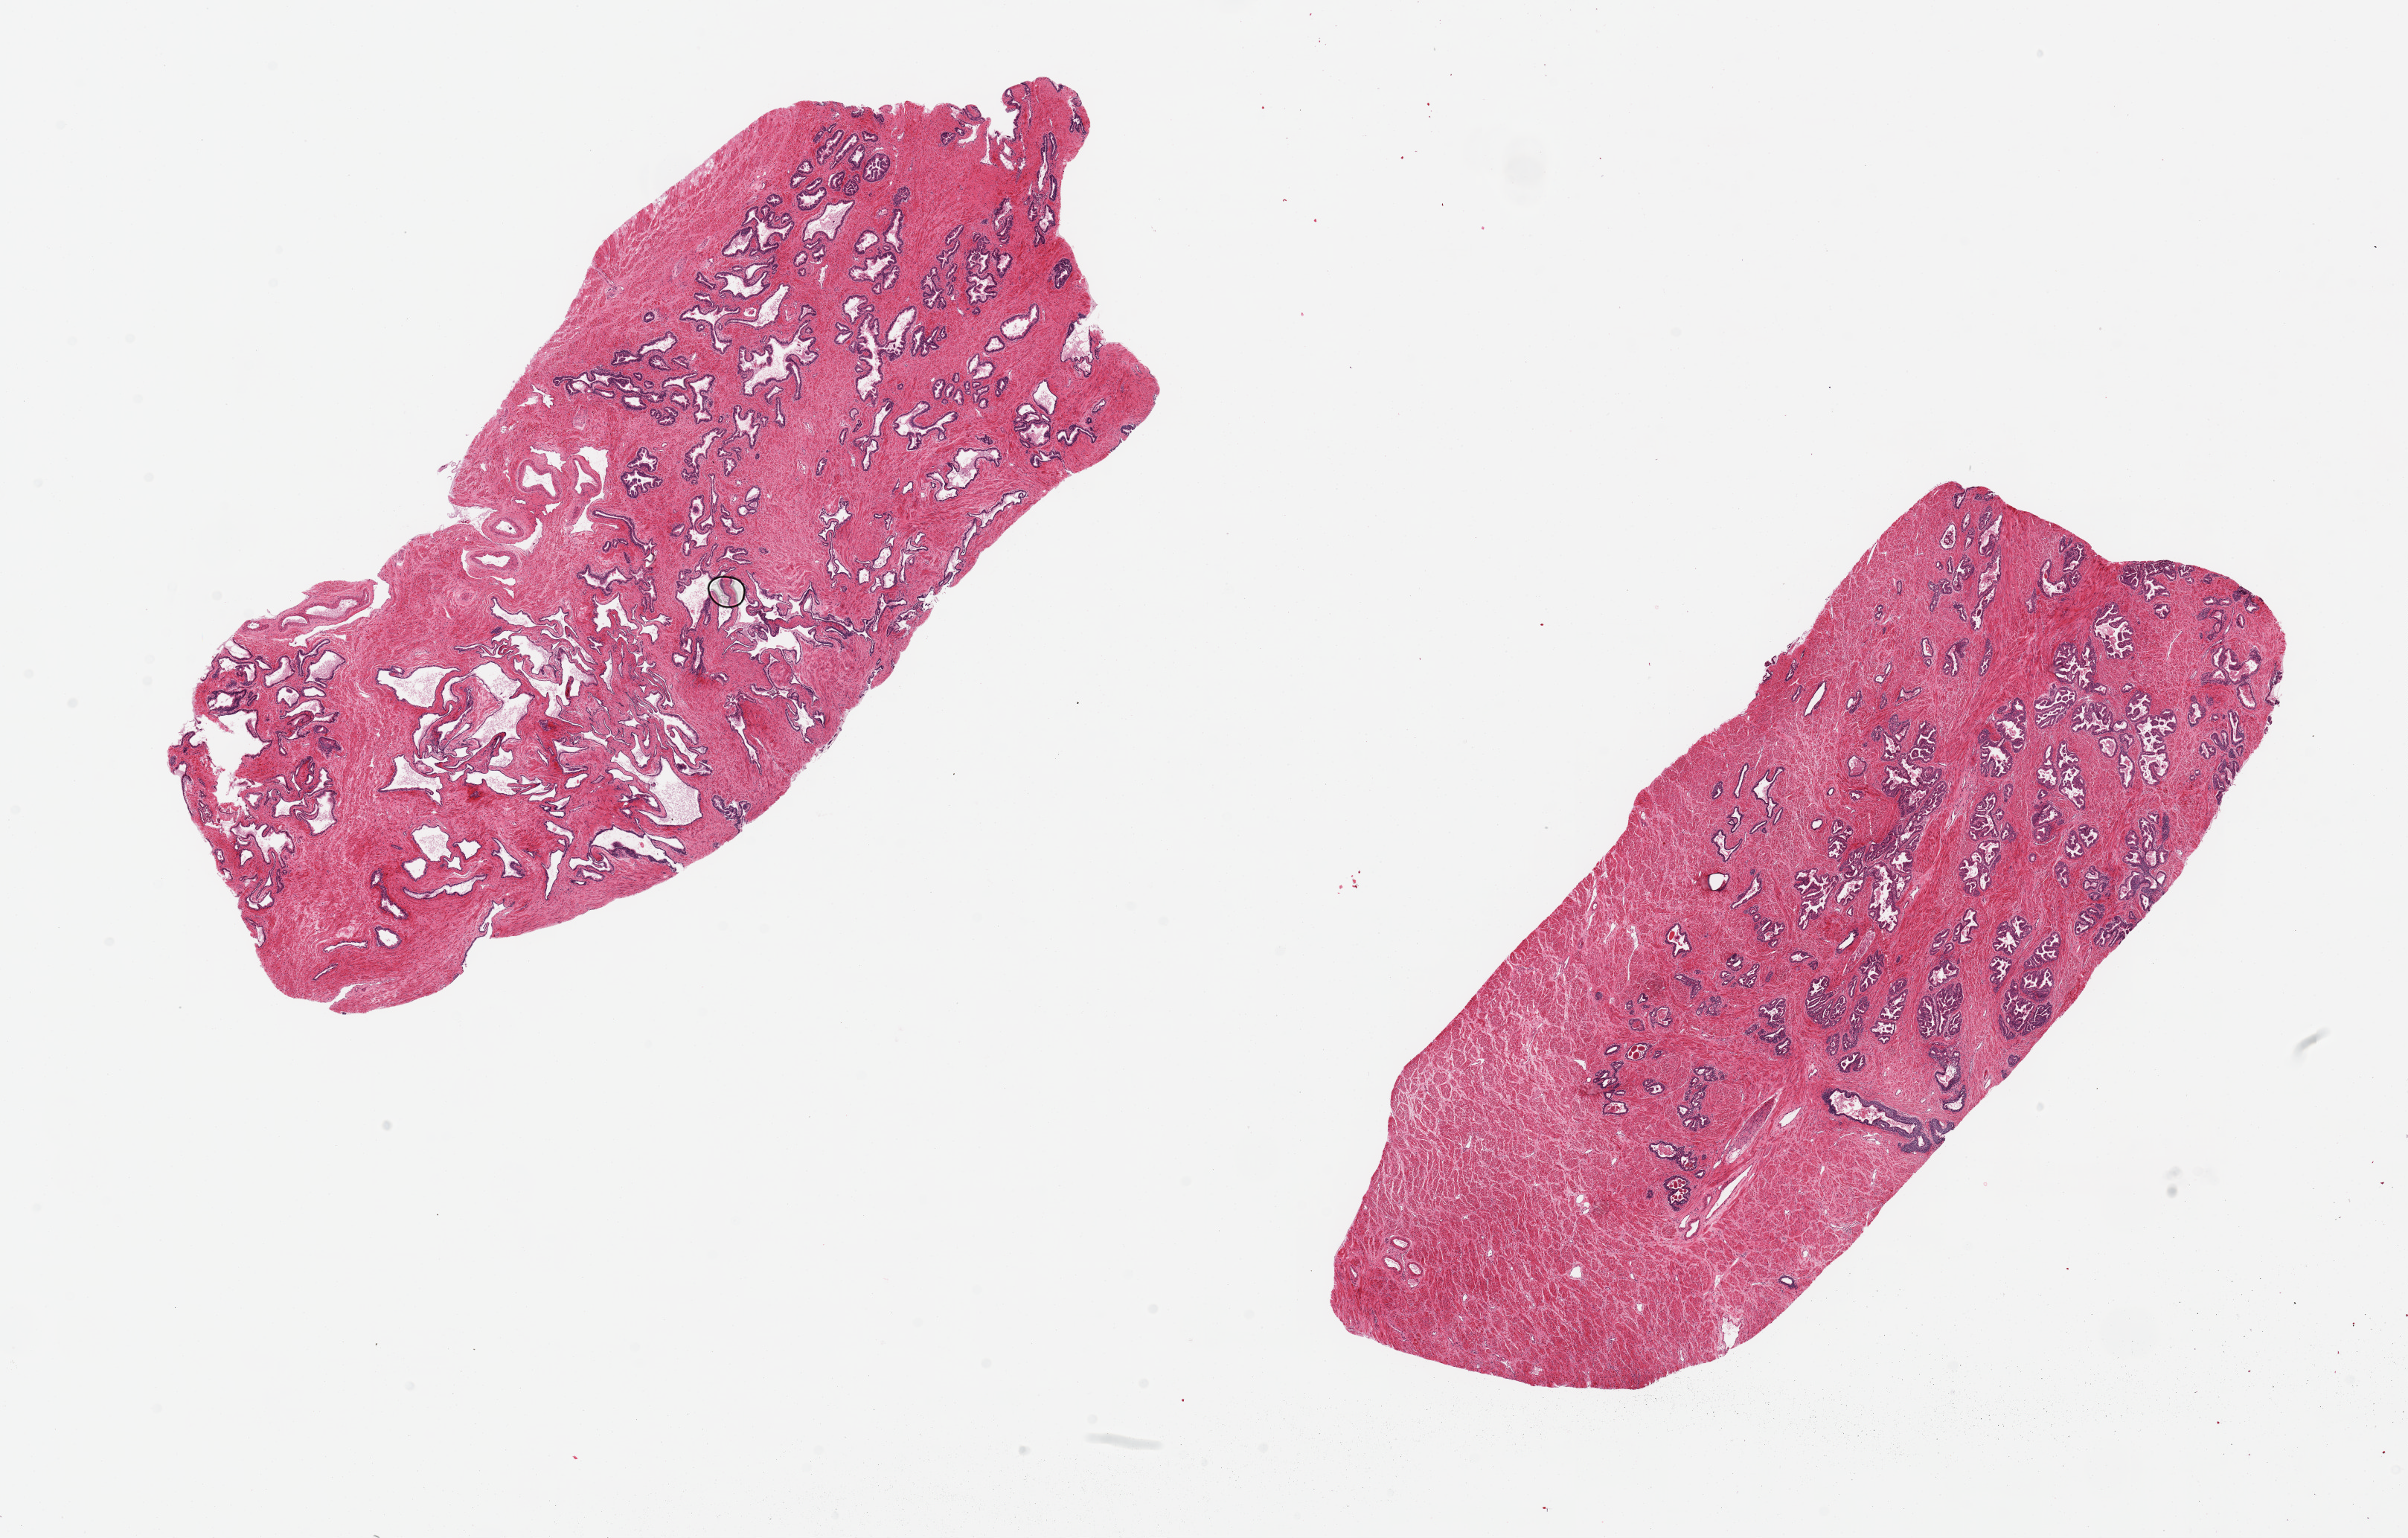
Hematoxylin and eosin (H&E) whole-slide image — shown as a low-resolution overview of the whole scanned area (about 25.6 x 16.3 mm), PAXgene-fixed paraffin-embedded (PFPE) section, sampled site (target tissue): prostate, tissue donor sample. Donor sex: male.
- review note (as recorded): 2 pieces ~11x5mm, patchy glandular hyperplasia and atrophy. Remarkably well-preserved glands